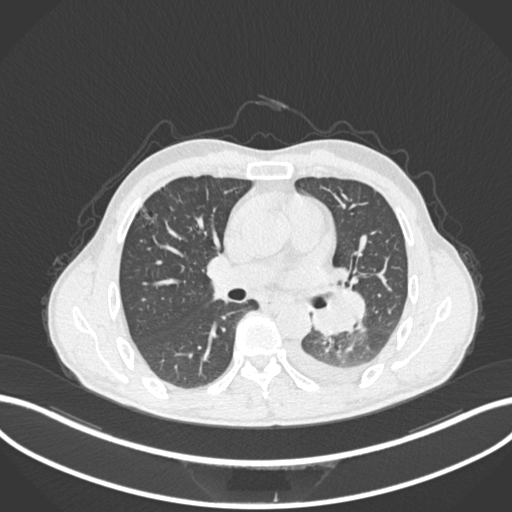
Chest CT, one axial slice. Slice 135 of 222 in the series (ordered by position). 120 kVp. Lung window (W 1500 / L -600 HU). 512 × 512 image matrix, field of view 400 × 400 mm. Male patient, age 47 years. Case-level facts recorded for this patient, not image findings: clinical TNM (as recorded): T3 N1 M1c.
Annotated regions visible in this slice (bounding box drawn by a radiologist):
- lung tumour (recorded histology: small cell carcinoma): box from (x=310, y=288) to (x=367, y=338) px